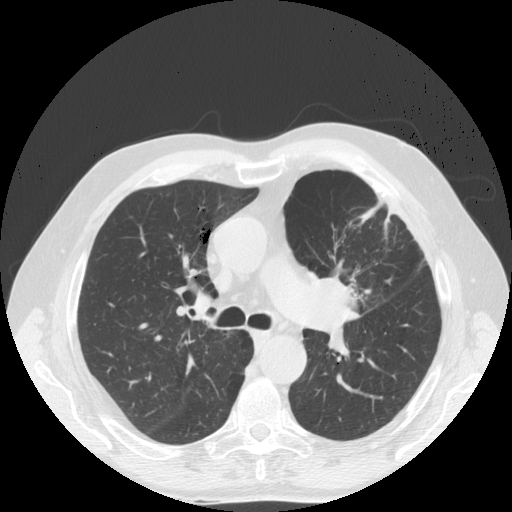
Low-dose screening chest CT, one axial slice; slice 113 of 170 in the series (ordered by position); 140 kVp; lung window (W 1500 / L -600 HU); 2.5 mm slice thickness; 512 × 512 image matrix, field of view 380 × 380 mm.
Annotated regions visible in this slice (outlined manually by an expert reader):
- lesion 1 (tumor, upper lobe of left lung): box from (x=316, y=274) to (x=362, y=316) px